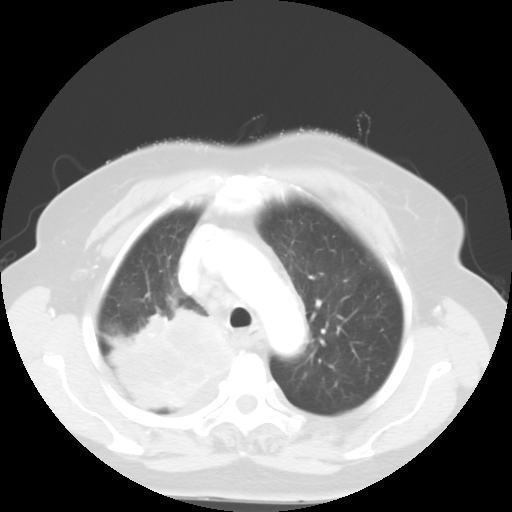
Chest CT, one axial slice; 120 kVp; lung window (W 1500 / L -600 HU); 512 × 512 image matrix, field of view 333 × 333 mm. Patient: female, 81 years. From the clinical record (not read from this slice): clinical TNM (as recorded): T4 N3 M1b.
Outlined on this slice (bounding box drawn by a radiologist):
- lung tumour (recorded histology: adenocarcinoma): bounding box <110,307,236,417> (left, top, right, bottom; pixels)